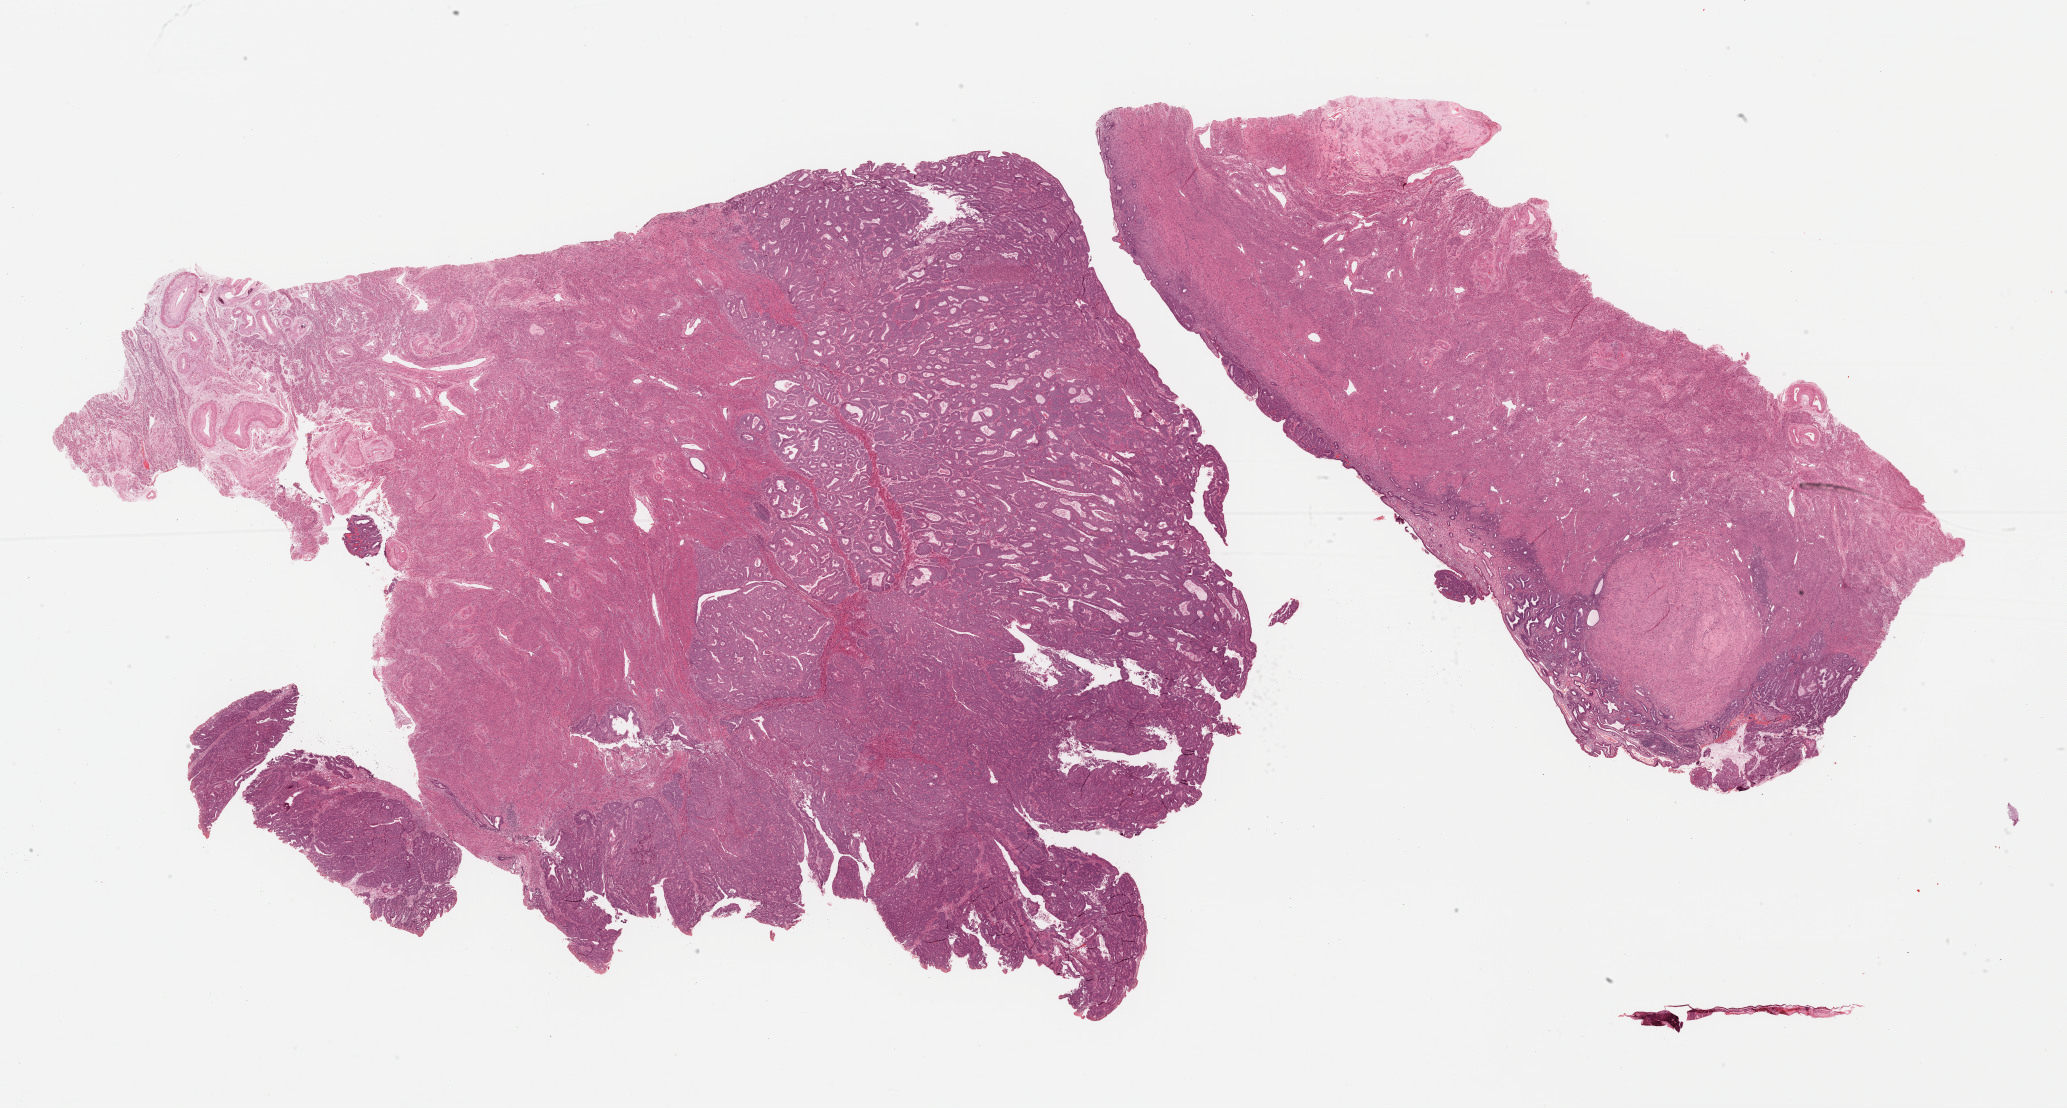
Whole-slide histology image, Hematoxylin and eosin (H&E) stained, shown as a low-resolution overview of the whole scanned area (about 32.7 x 17.5 mm, acquisition: 40x scan); formalin-fixed paraffin-embedded (FFPE) diagnostic section; primary tumour sample from the uterus. Female patient; age at initial diagnosis 81 years. Histologic grade: G2 (moderately differentiated).
FIGO stage: IIA. Diagnosis: Endometrioid adenocarcinoma, NOS.